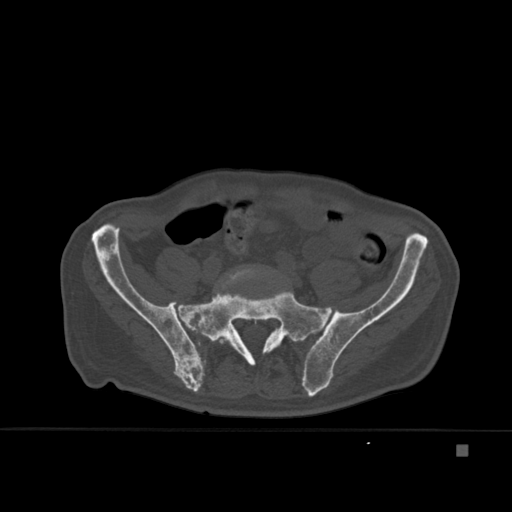
CT including the spine, one axial slice. Slice 90 of 451 in the series (ordered by position). Bone window (W 1800 / L 400 HU). 1.5 mm slice thickness. 512 × 512 image matrix, field of view 378 × 378 mm. Patient: male, 75 years. Case-level facts recorded for this patient, not image findings: primary cancer: prostate.
Outlined on this slice (semi-automatic segmentation, software-assisted and operator-edited):
- L5 vertebra: bounding box <219,265,259,349> (left, top, right, bottom; pixels)